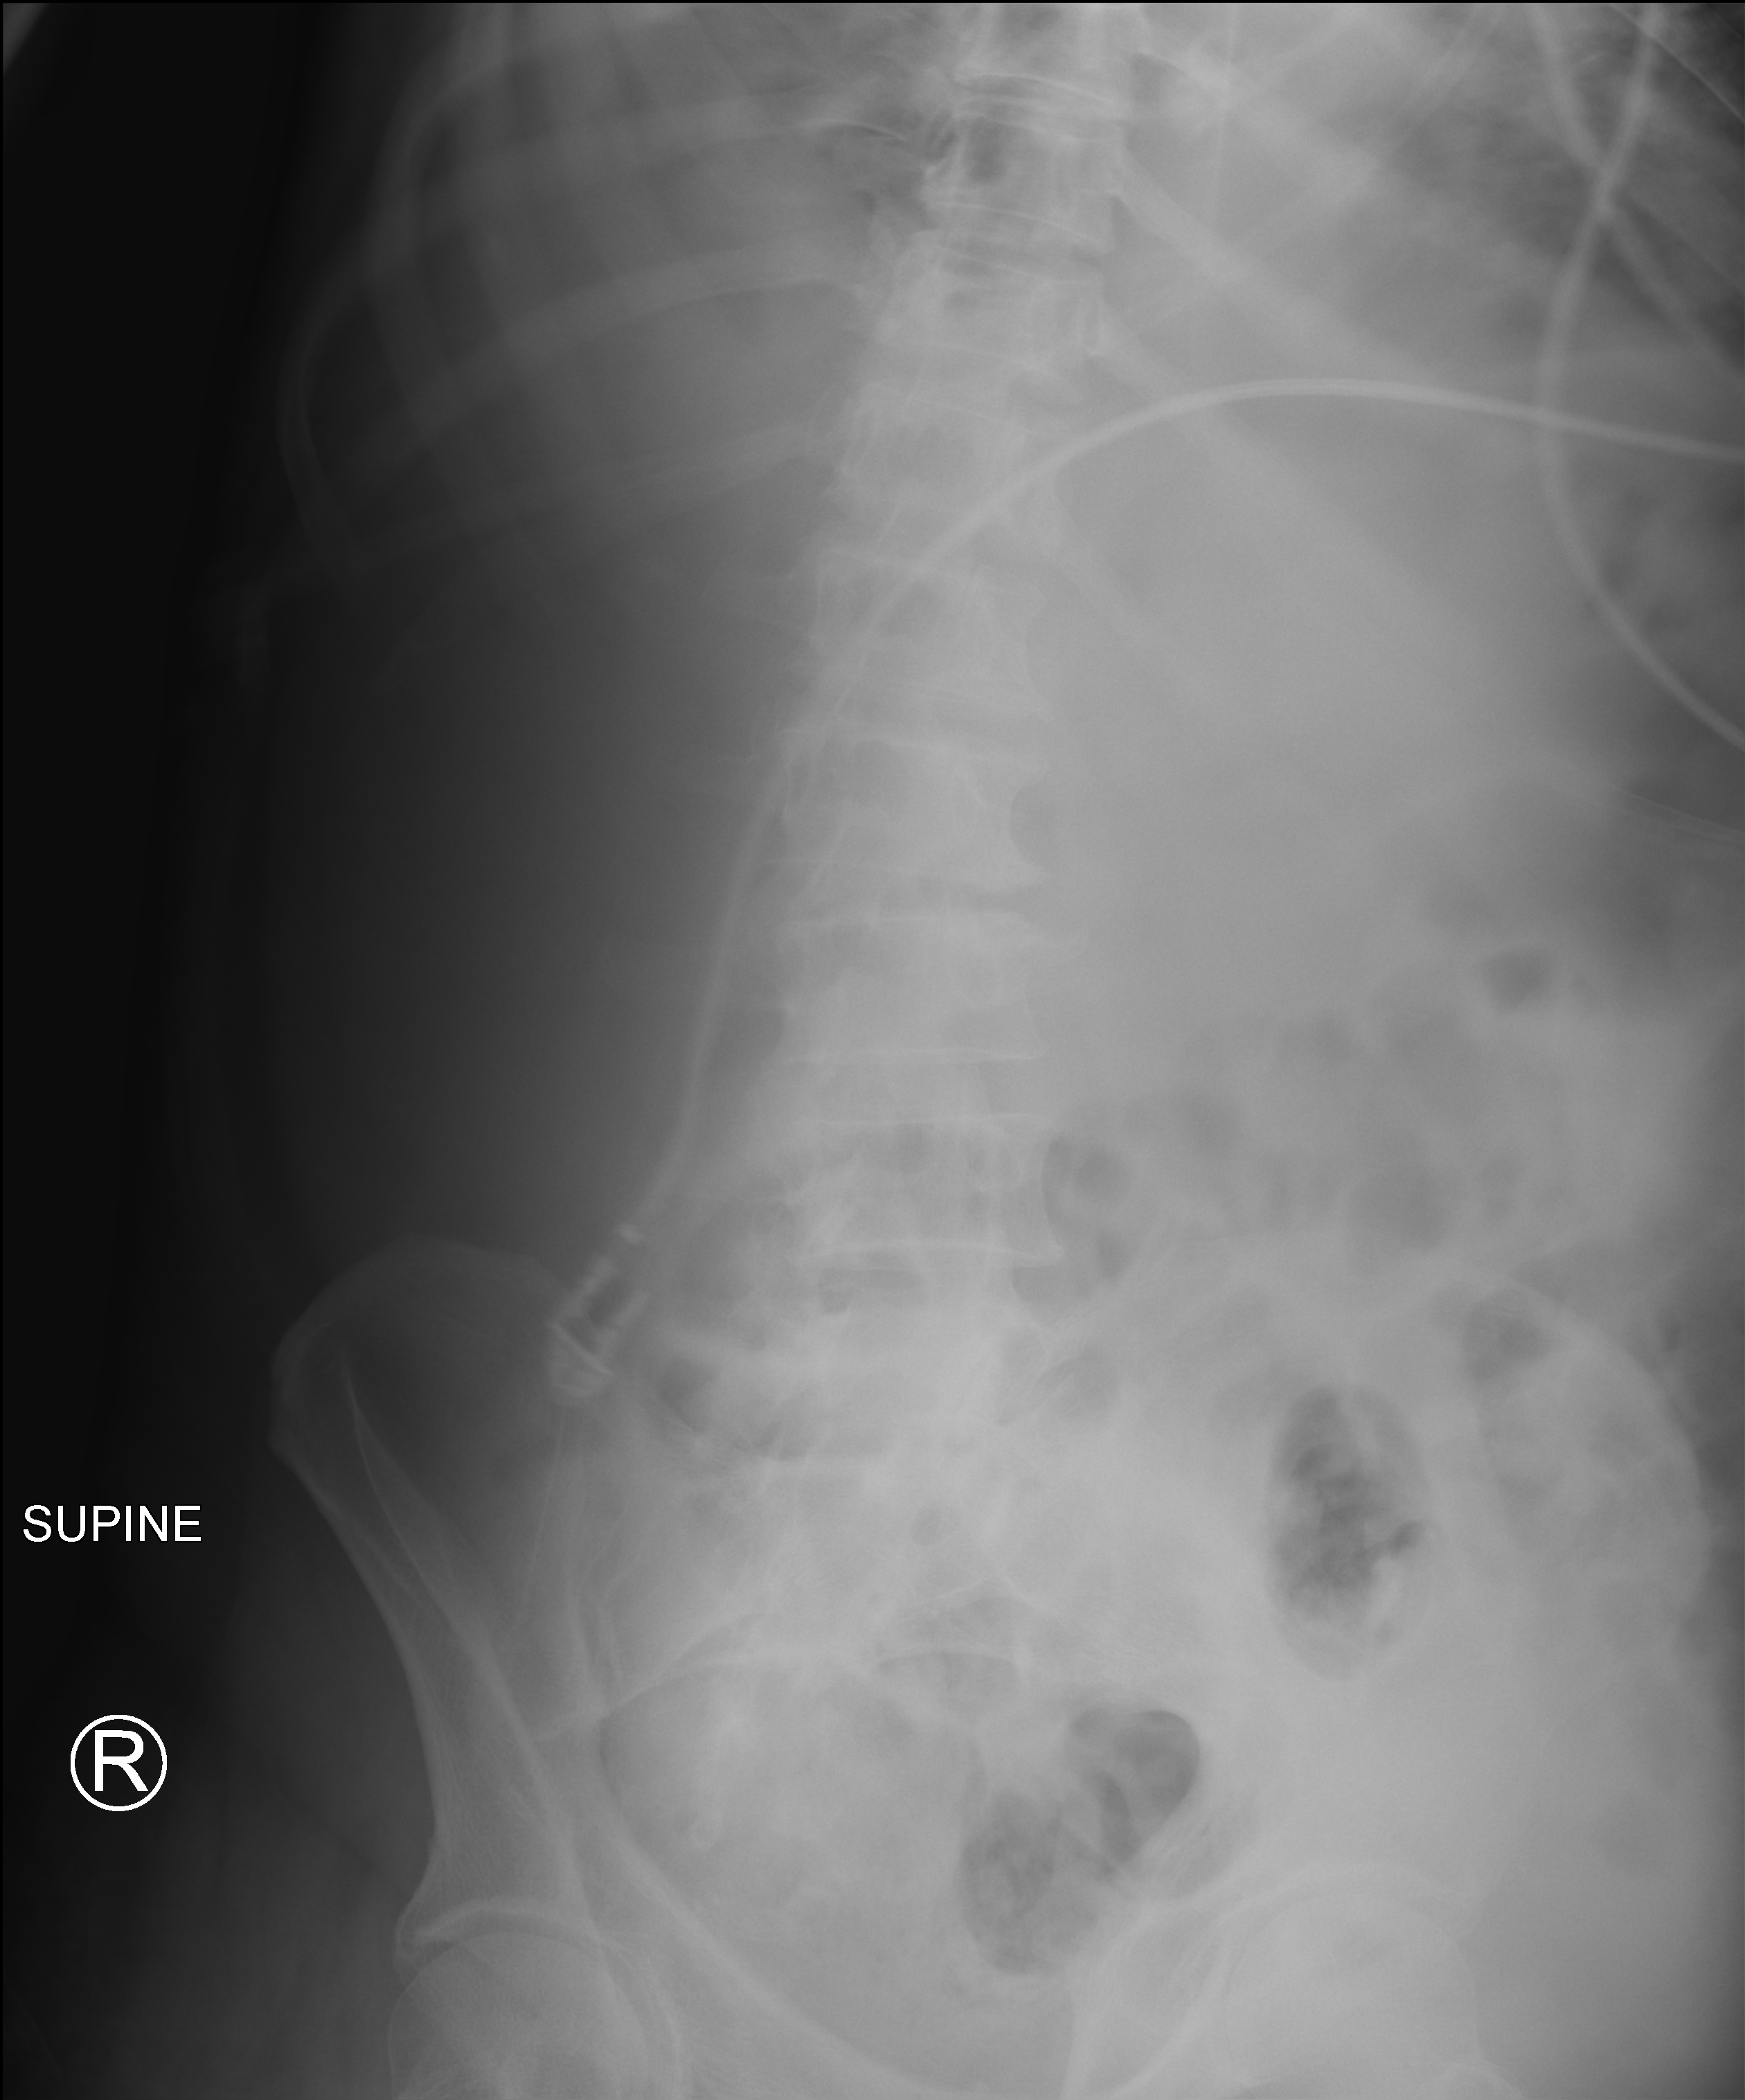
Bedside abdomen radiograph (computed radiography); anteroposterior (AP) projection. Patient hospitalised with COVID-19; male, aged 75–90 years.
From the hospital-stay record, not from the radiograph (when in the stay this image was taken is not recorded):
- mechanically ventilated during this hospital stay: yes
- admitted to intensive care during this hospital stay: yes